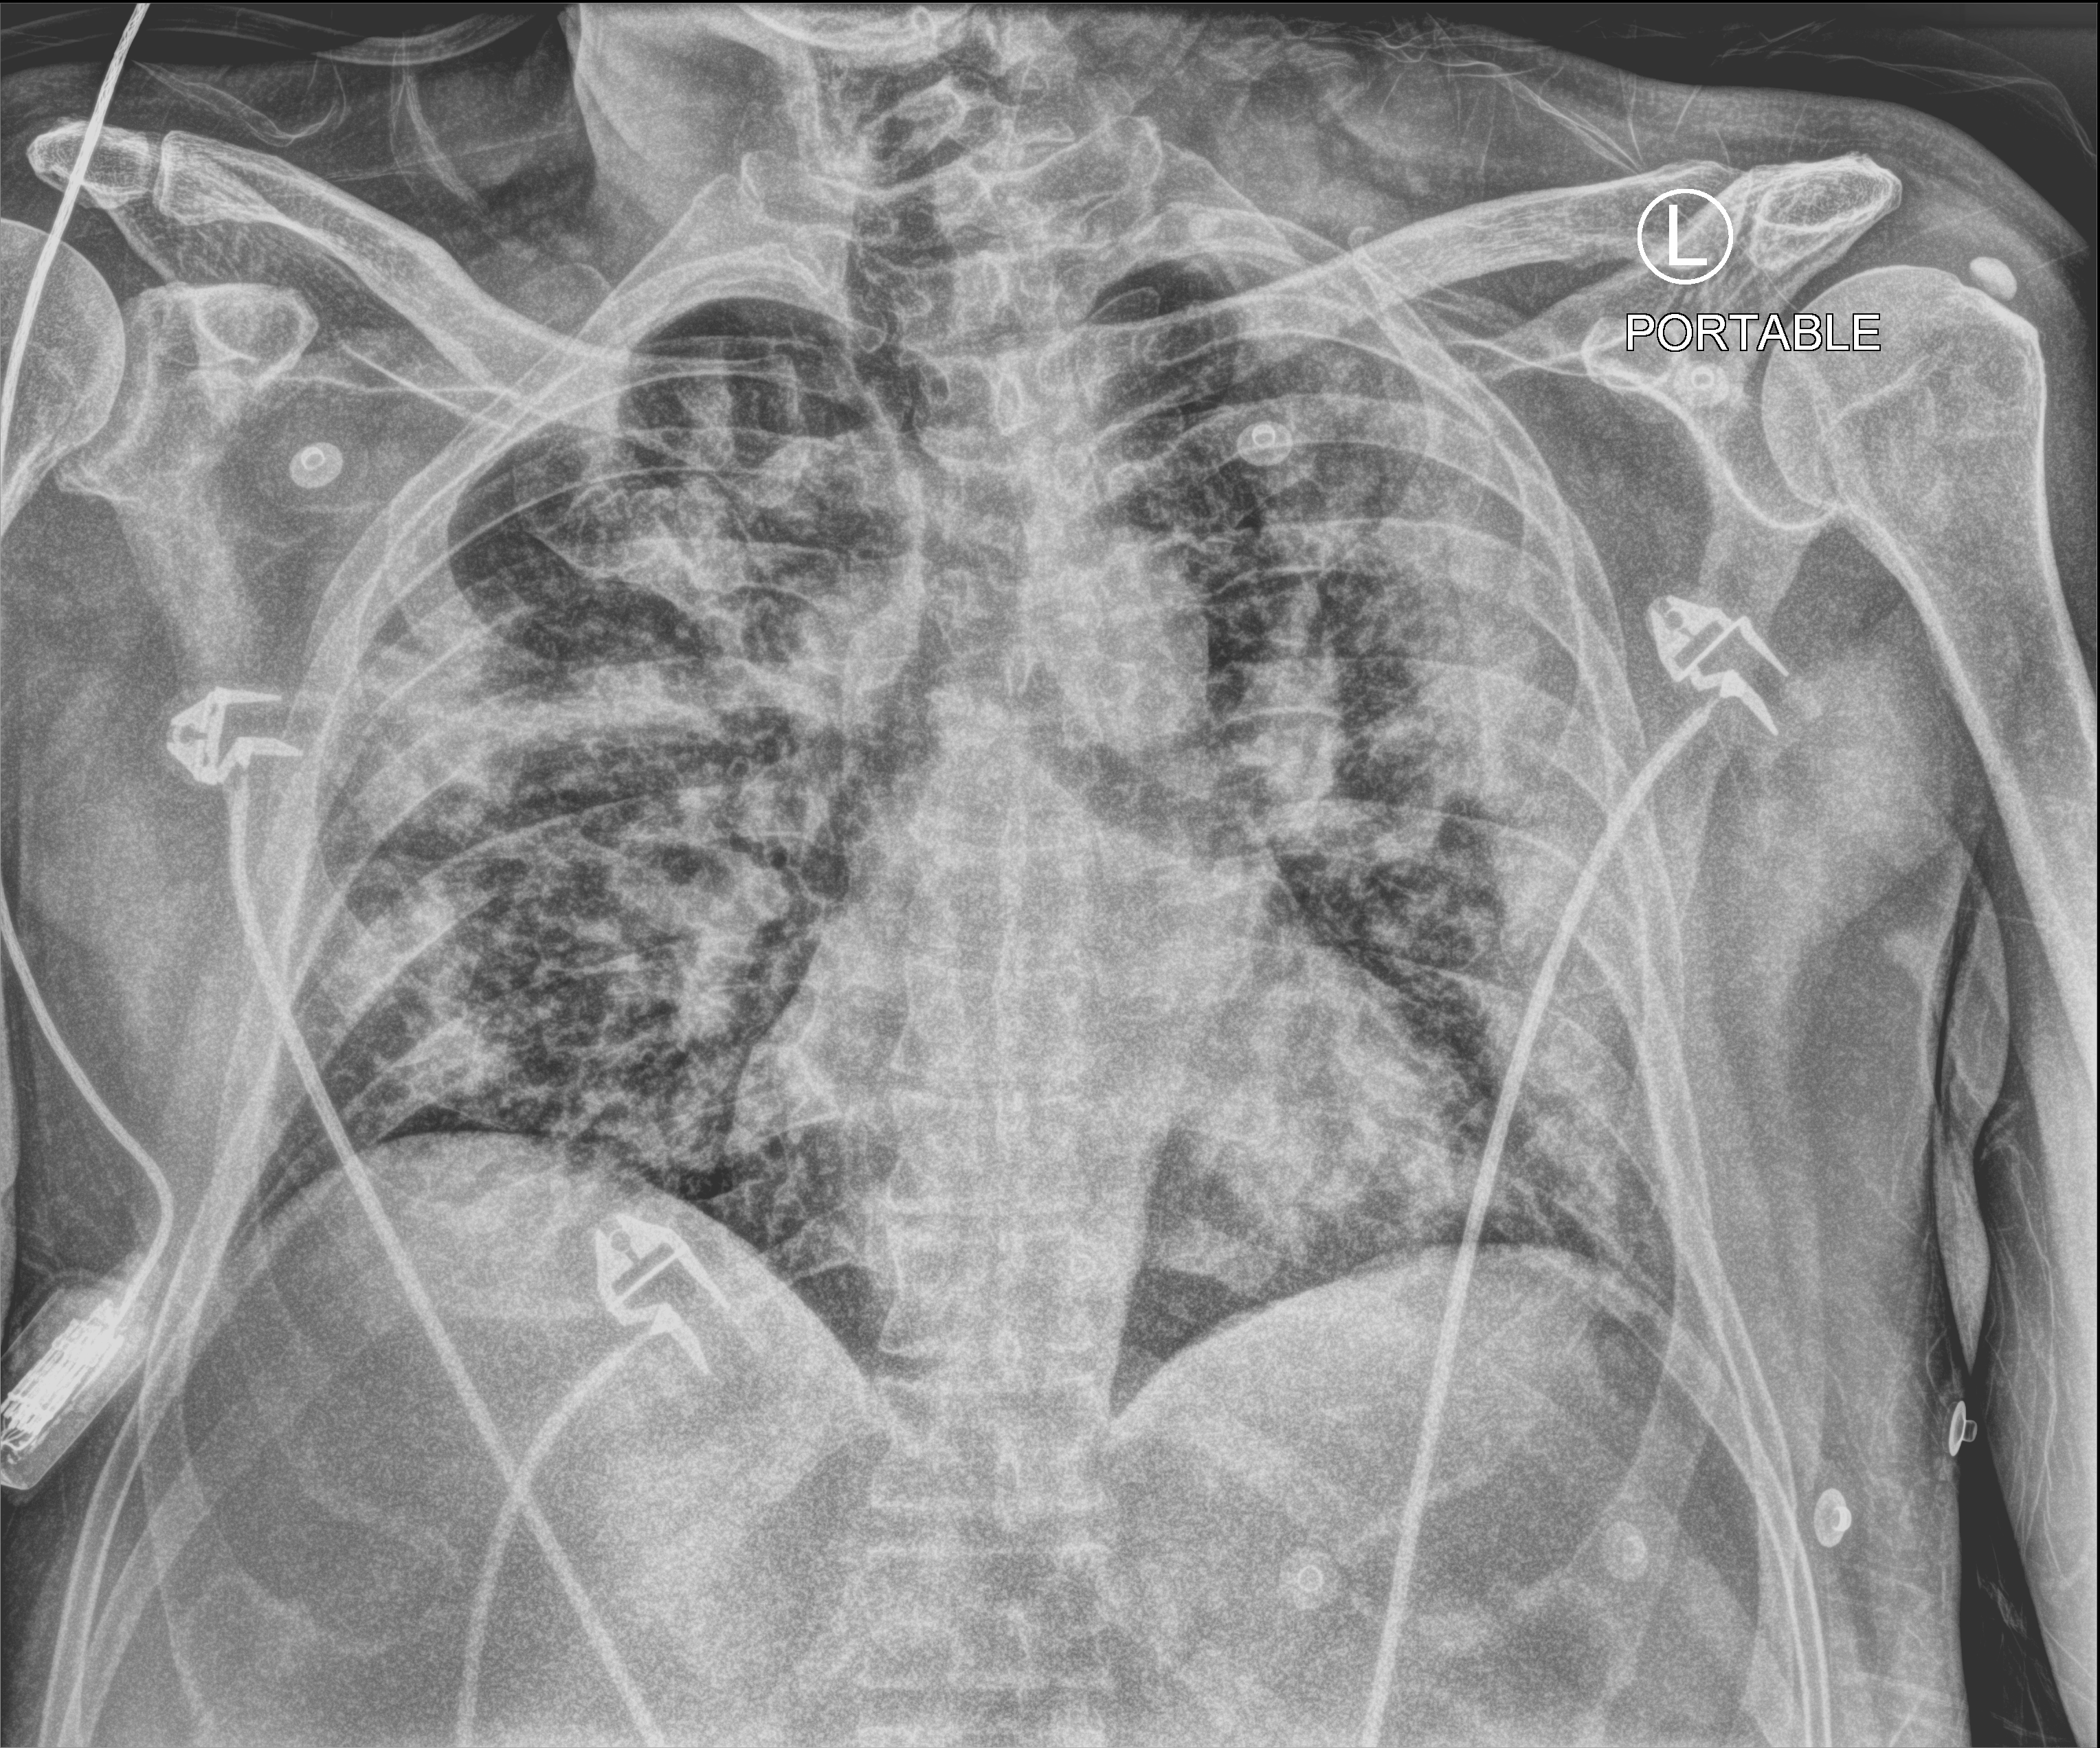
Portable chest radiograph, anteroposterior (AP) projection. Male patient hospitalised with COVID-19, age 18–59 years.
Hospital-stay facts (about this admission, not read from this image; timing relative to this image not recorded): mechanically ventilated during this hospital stay: yes; length of hospital stay: 25 days.